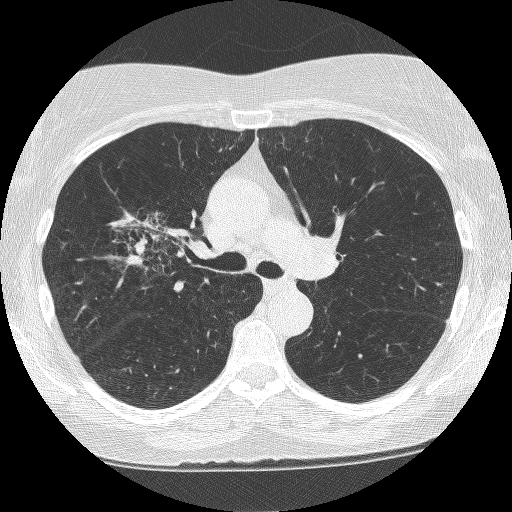
Axial slice from a low-dose chest CT screening exam; second screening round (one year after baseline); lung window (W 1500 / L -600 HU); 1.25 mm slice thickness; slice 158 of 249 in the series. Female, age 64 years at enrolment. Former smoker at enrolment.
• Expert reader's lesion annotation, bounding box [x1, y1, x2, y2] px = [115, 205, 207, 292].
• The screening reader recorded 4 non-calcified nodules or masses ≥4 mm on this exam (right upper lobe, right upper lobe, right upper lobe, left upper lobe); which of them this box marks is not recorded.
• Official screen result: positive, other.
• Participant outcome: lung cancer diagnosed 381 days after this screen (after the third annual screen) — adenocarcinoma, NOS, right upper lobe, right middle lobe, right hilum, stage IV (AJCC 6th edition), 85 mm at pathology.